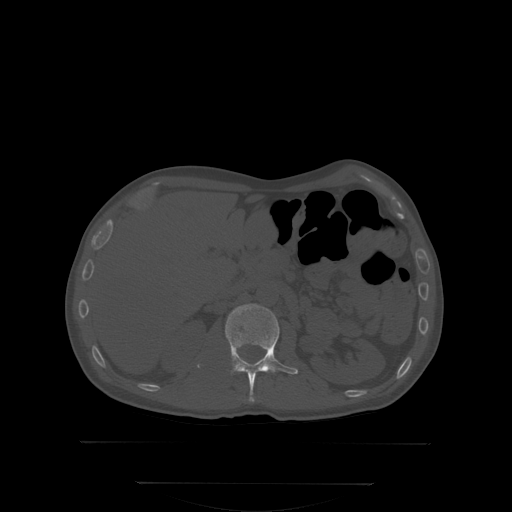
CT including the spine, one axial slice. Slice 153 of 350 in the series (ordered by position). Bone window (W 1800 / L 400 HU). 2.5 mm slice thickness. 512 × 512 image matrix. Patient: male, 58 years. From the clinical record (not read from this slice): primary cancer: prostate.
Annotated regions visible in this slice (semi-automatic segmentation, software-assisted and operator-edited):
- L1 vertebra: bounding box (x1, y1, x2, y2) in pixels: (225, 304, 298, 401)